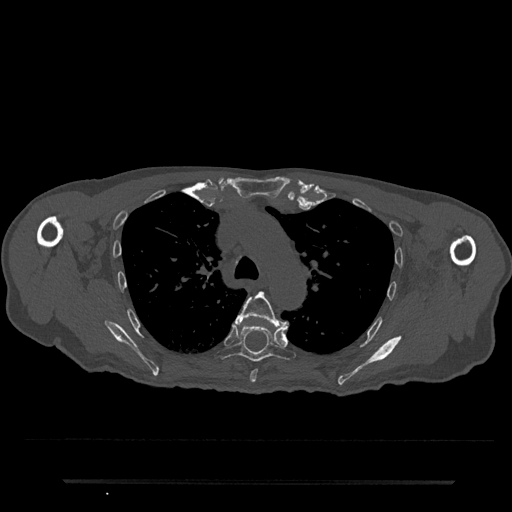
CT including the spine, one axial slice. Position 548 of 797 along the scan axis. 120 kVp. Bone window (W 1800 / L 400 HU). 0.5 mm slice thickness. 512 × 512 image matrix, field of view 427 × 427 mm. Patient: male, 74 years. From the clinical record (not read from this slice): primary cancer: prostate.
Structures marked on this image (semi-automatically segmented with operator editing):
- T5 vertebra: bounding box [x1, y1, x2, y2] px = [236, 291, 289, 383]
- T6 vertebra: [215, 318, 296, 362]